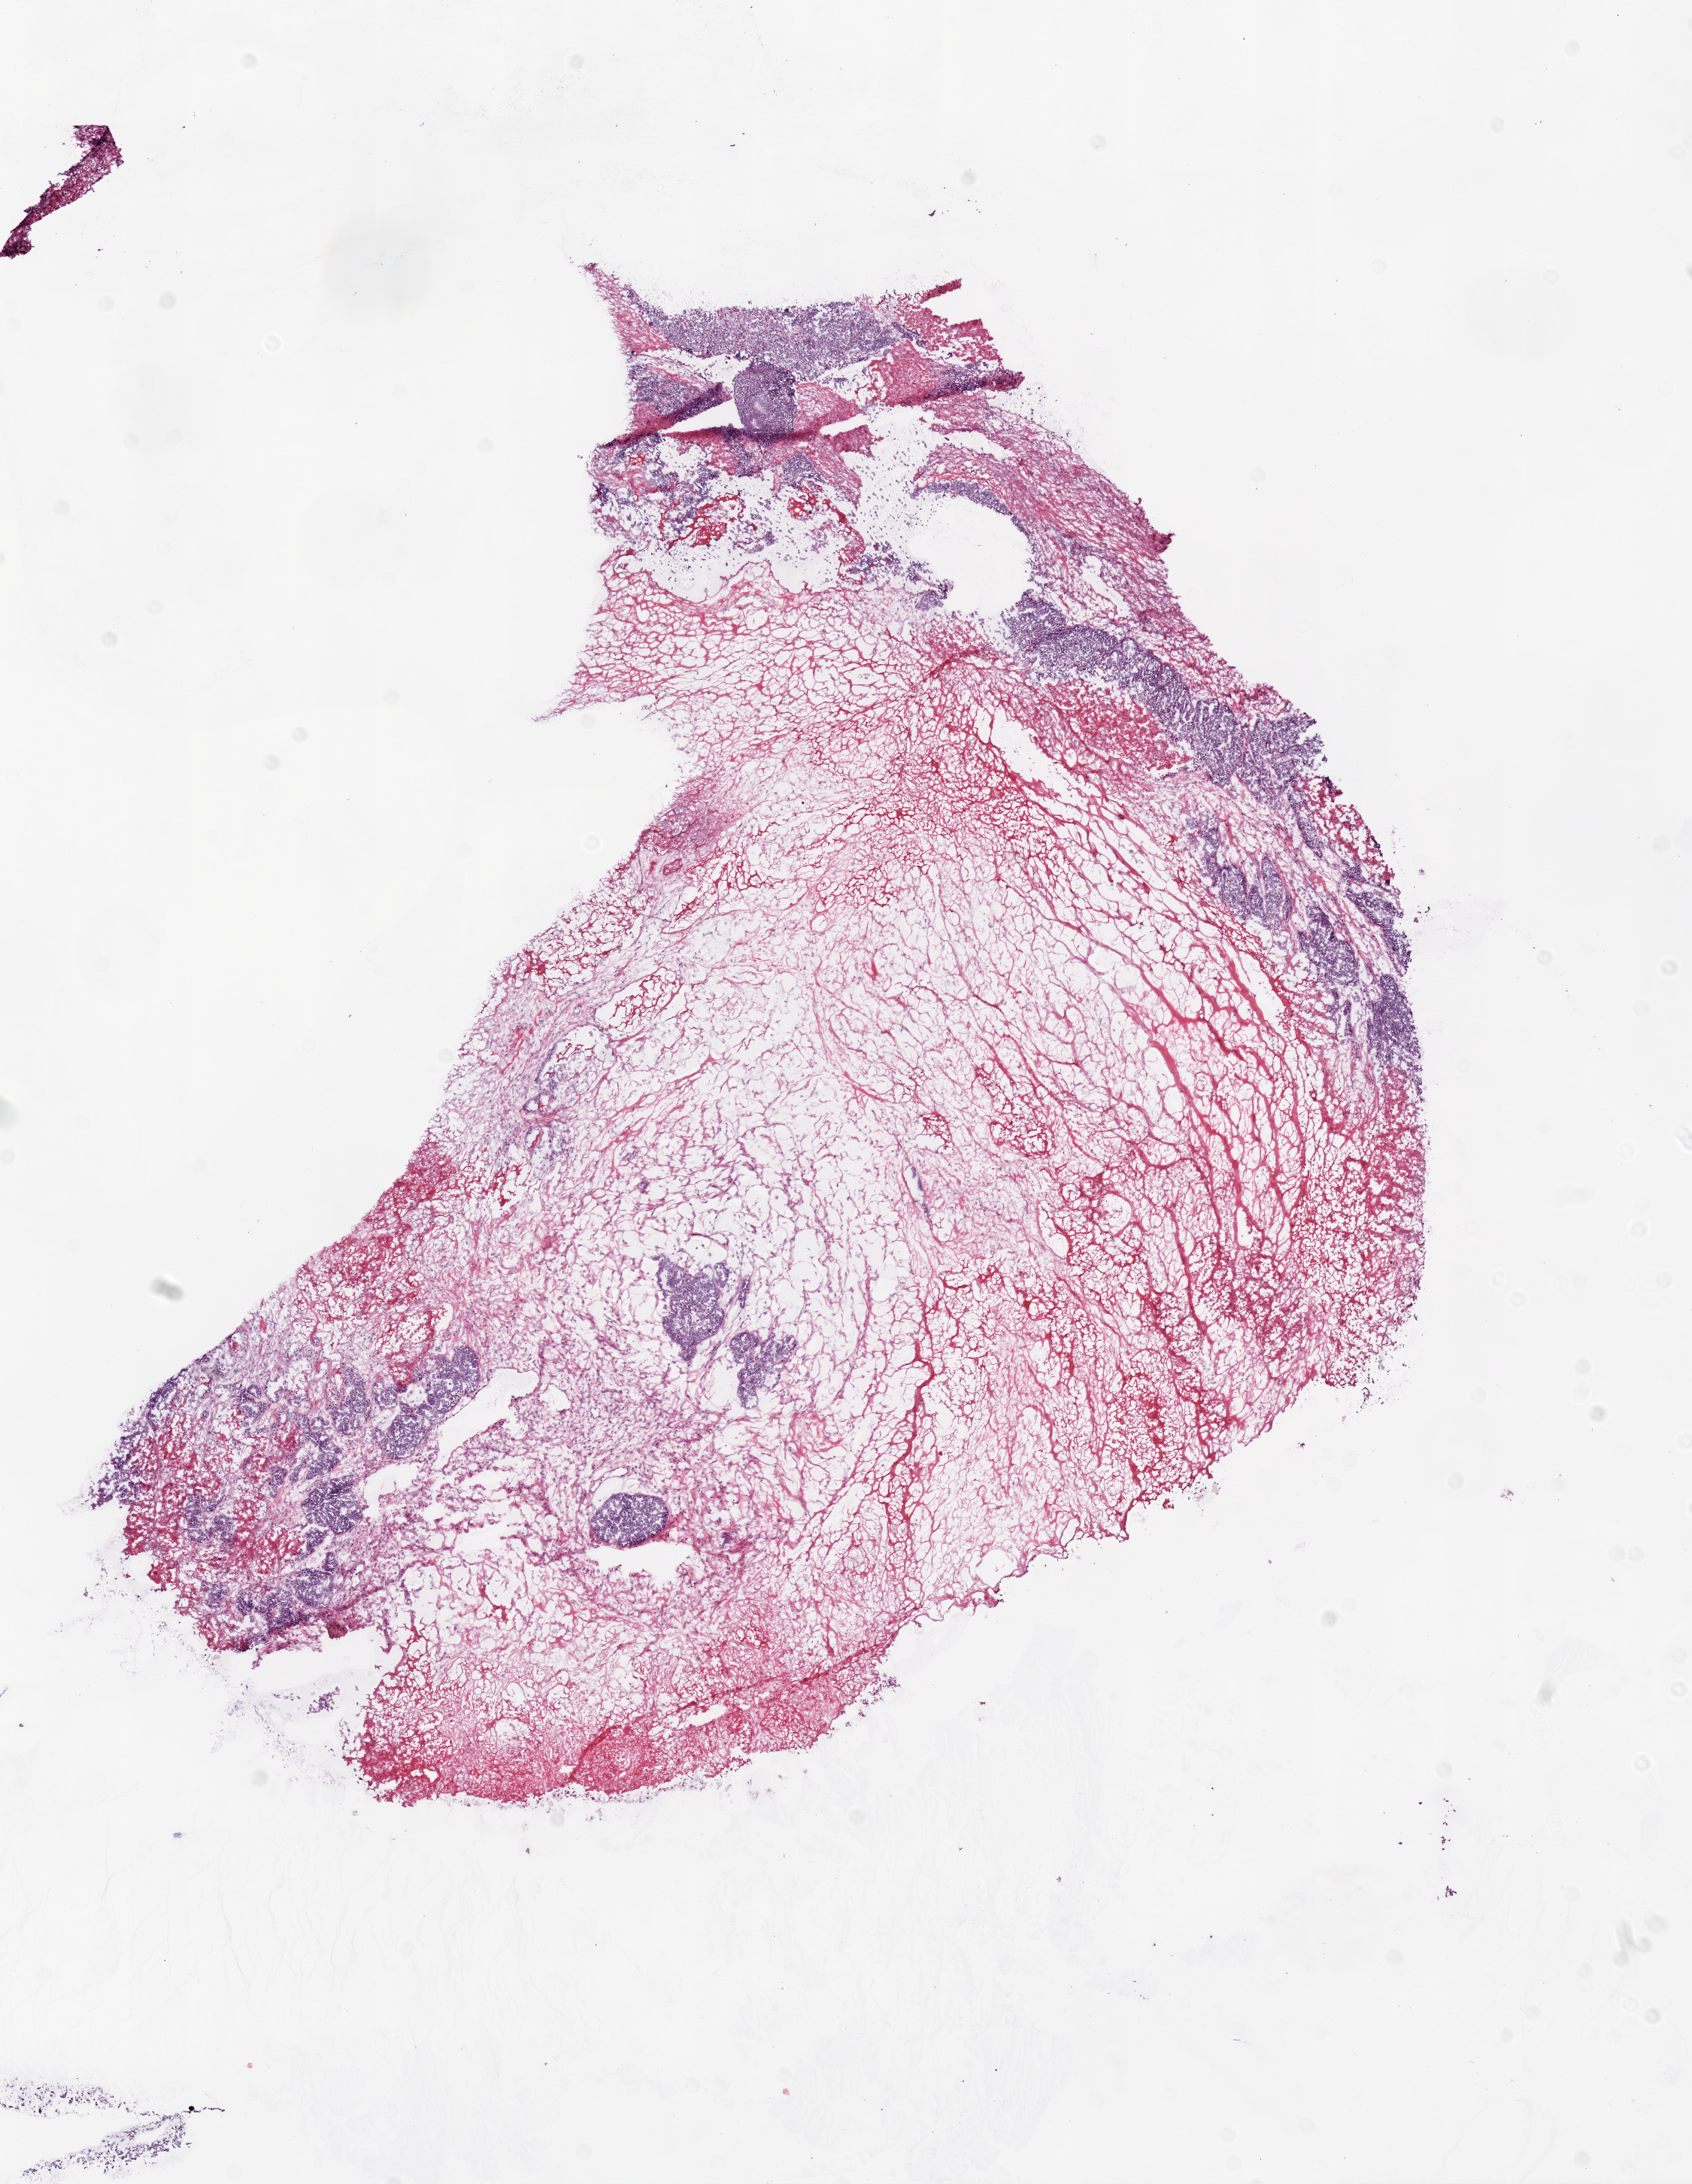
Whole-slide histology image, H&E-stained, shown as a low-resolution overview of the whole scanned area (about 9.0 x 11.7 mm, from a 20x scan), frozen section from the bottom of the tissue portion, sample: primary tumour, ovary. Female, age 48 years at initial diagnosis. Histologic grade: G3 (poorly differentiated). Pathologist review of this section (percent, as recorded): tumour cells 8%, tumour nuclei 90%, normal cells 15%, stromal cells 72%, necrosis 5%.
- pathologic diagnosis: Serous cystadenocarcinoma, NOS
- FIGO stage: IIIC